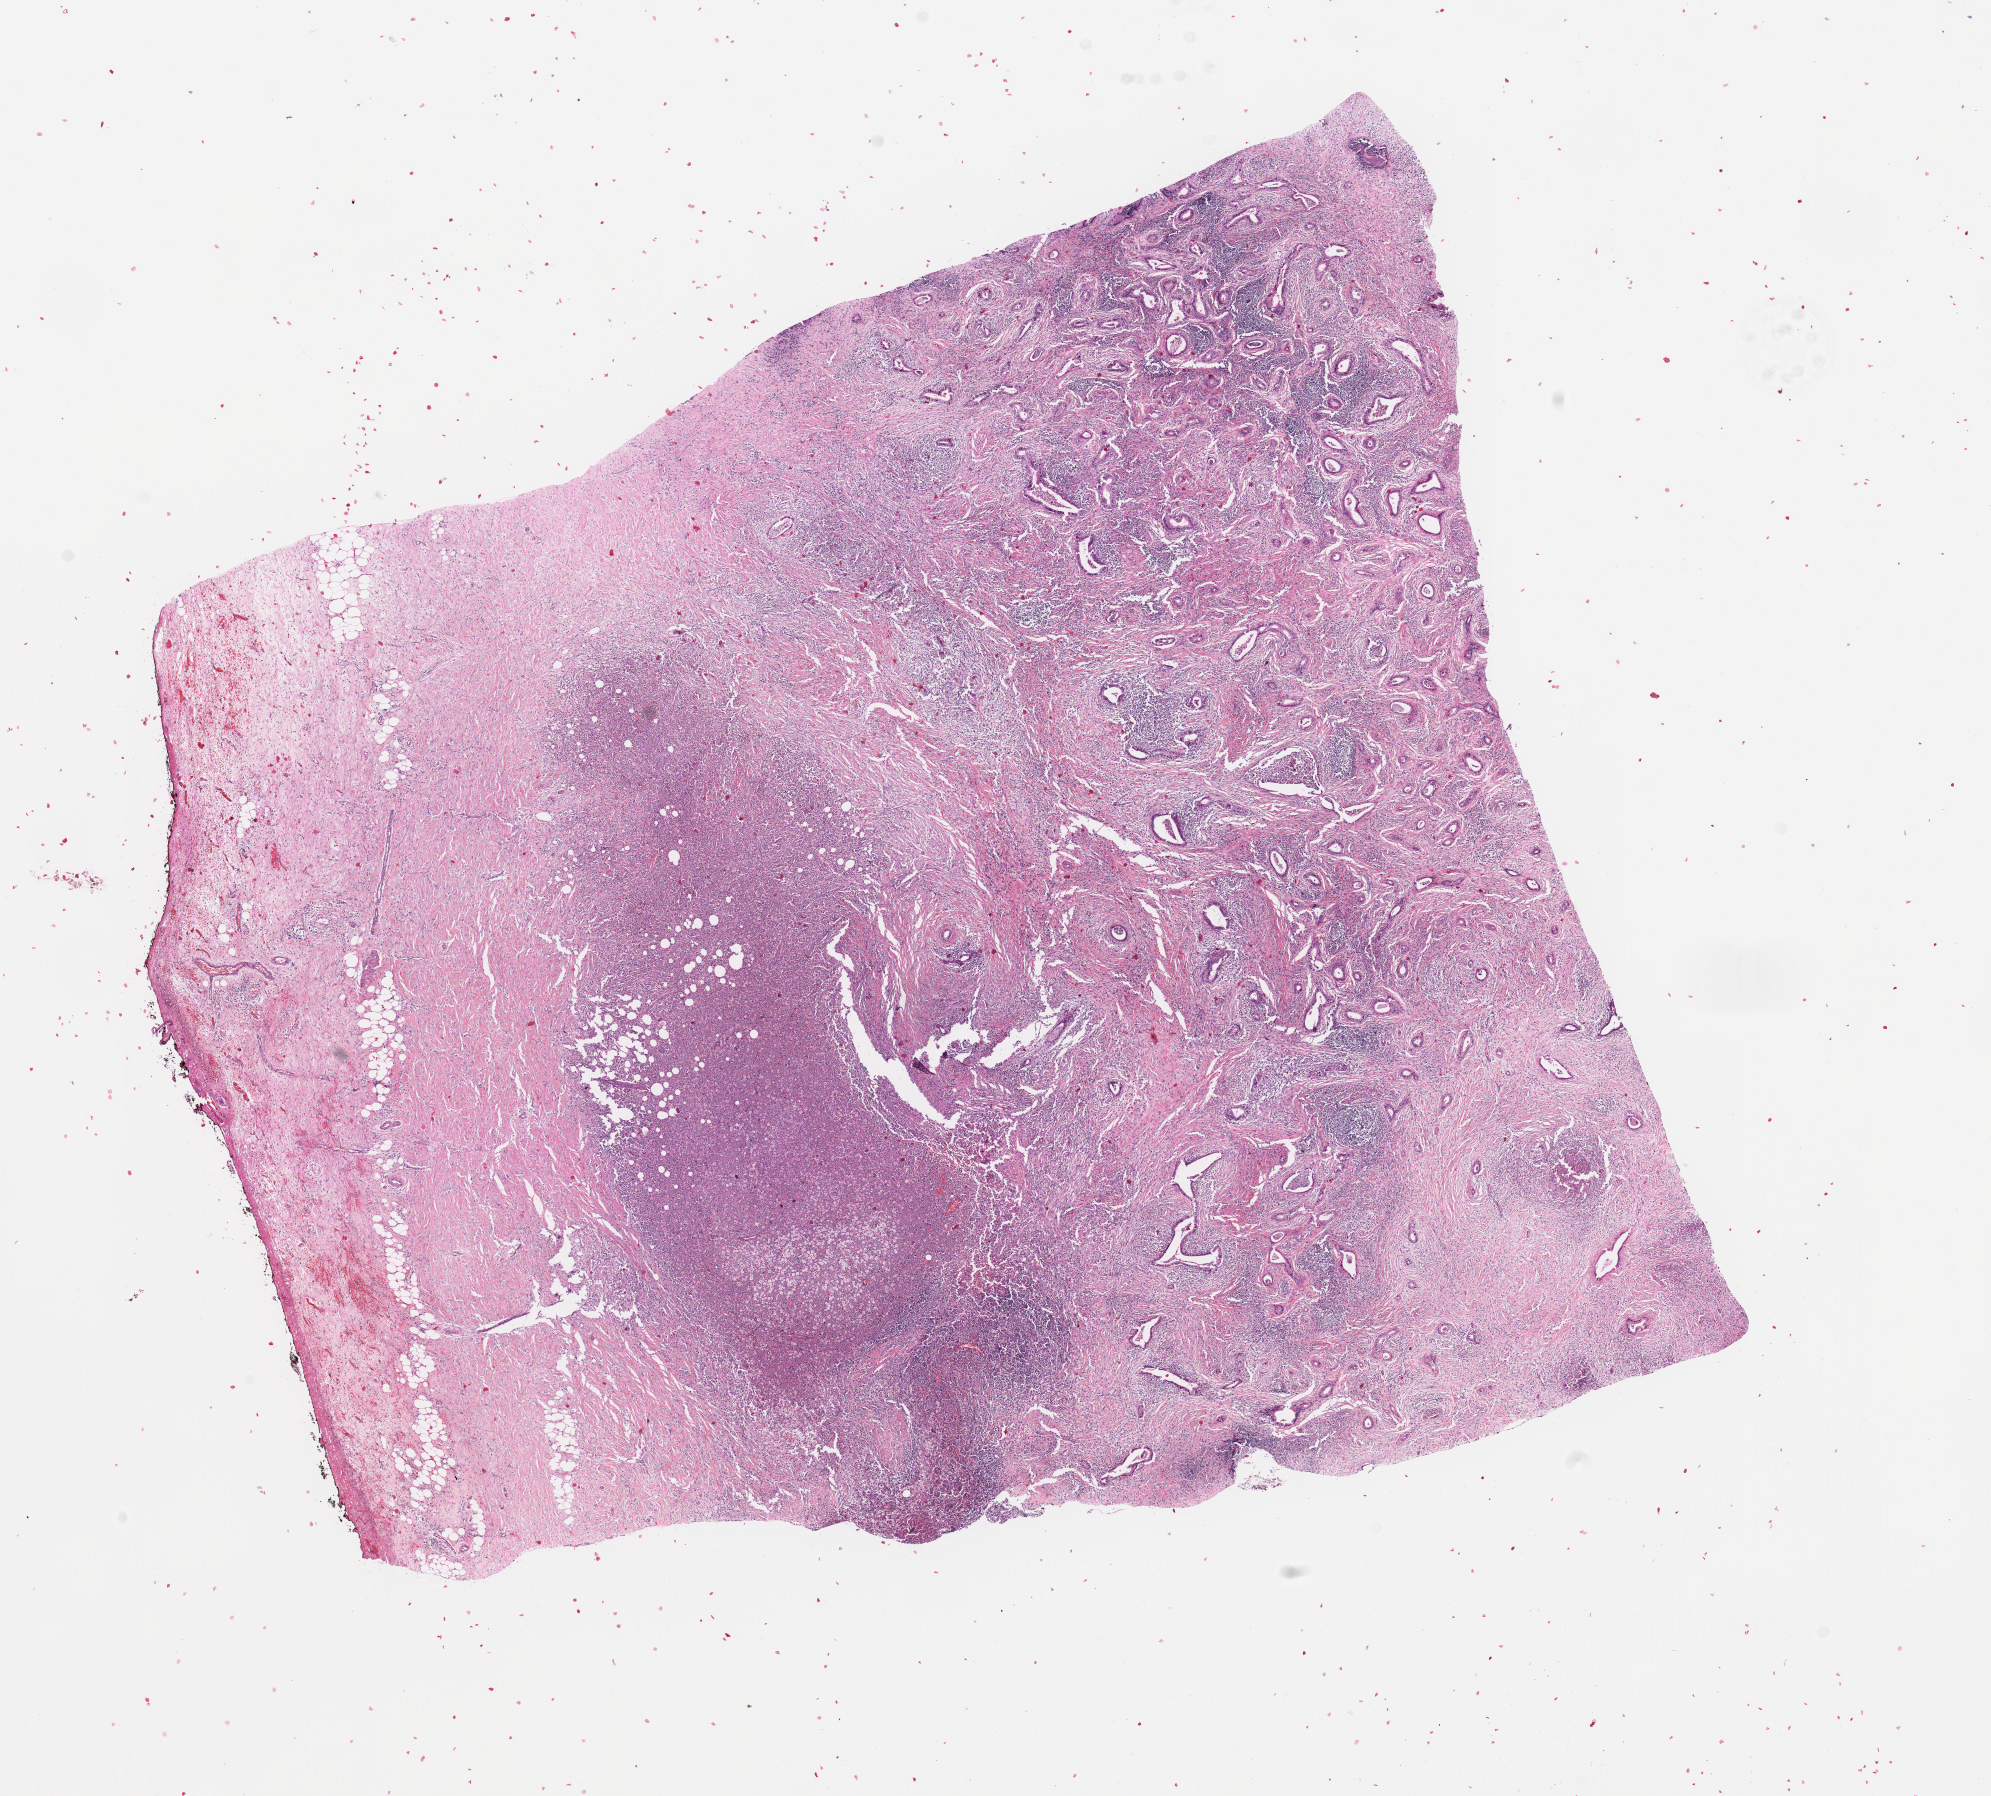
Digitized H&E-stained tissue section (whole slide), shown as a low-resolution overview of the whole scanned area (about 15.8 x 14.2 mm), tumour tissue sample, sampled site: pancreas. Patient: female, age 68 years. Histologic grade: G2 (moderately differentiated). Slide review estimates, as recorded: tumour nuclei 5%, necrosis 5%.
Histologic diagnosis: Infiltrating duct carcinoma, NOS. Primary tumour site (as recorded): head. AJCC pathologic stage: IB.